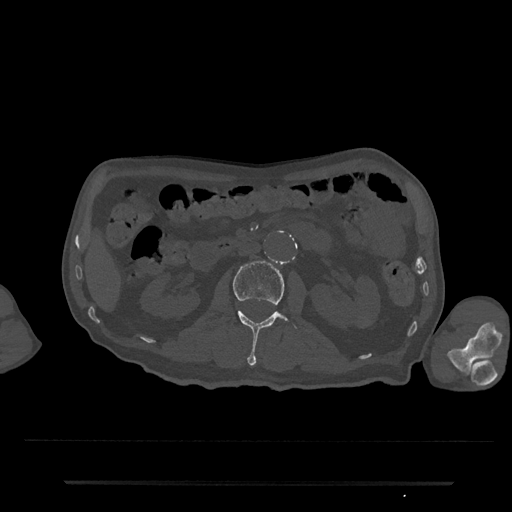
CT including the spine, one axial slice; reconstruction kernel Br40s/3; bone window (W 1800 / L 400 HU); 0.5 mm slice thickness; 512 × 512 image matrix. Male patient, age 74 years. Case-level facts recorded for this patient, not image findings: primary cancer: prostate.
Outlined on this slice (semi-automatically segmented with operator editing):
- L2 vertebra: box from (x=233, y=261) to (x=305, y=365) px